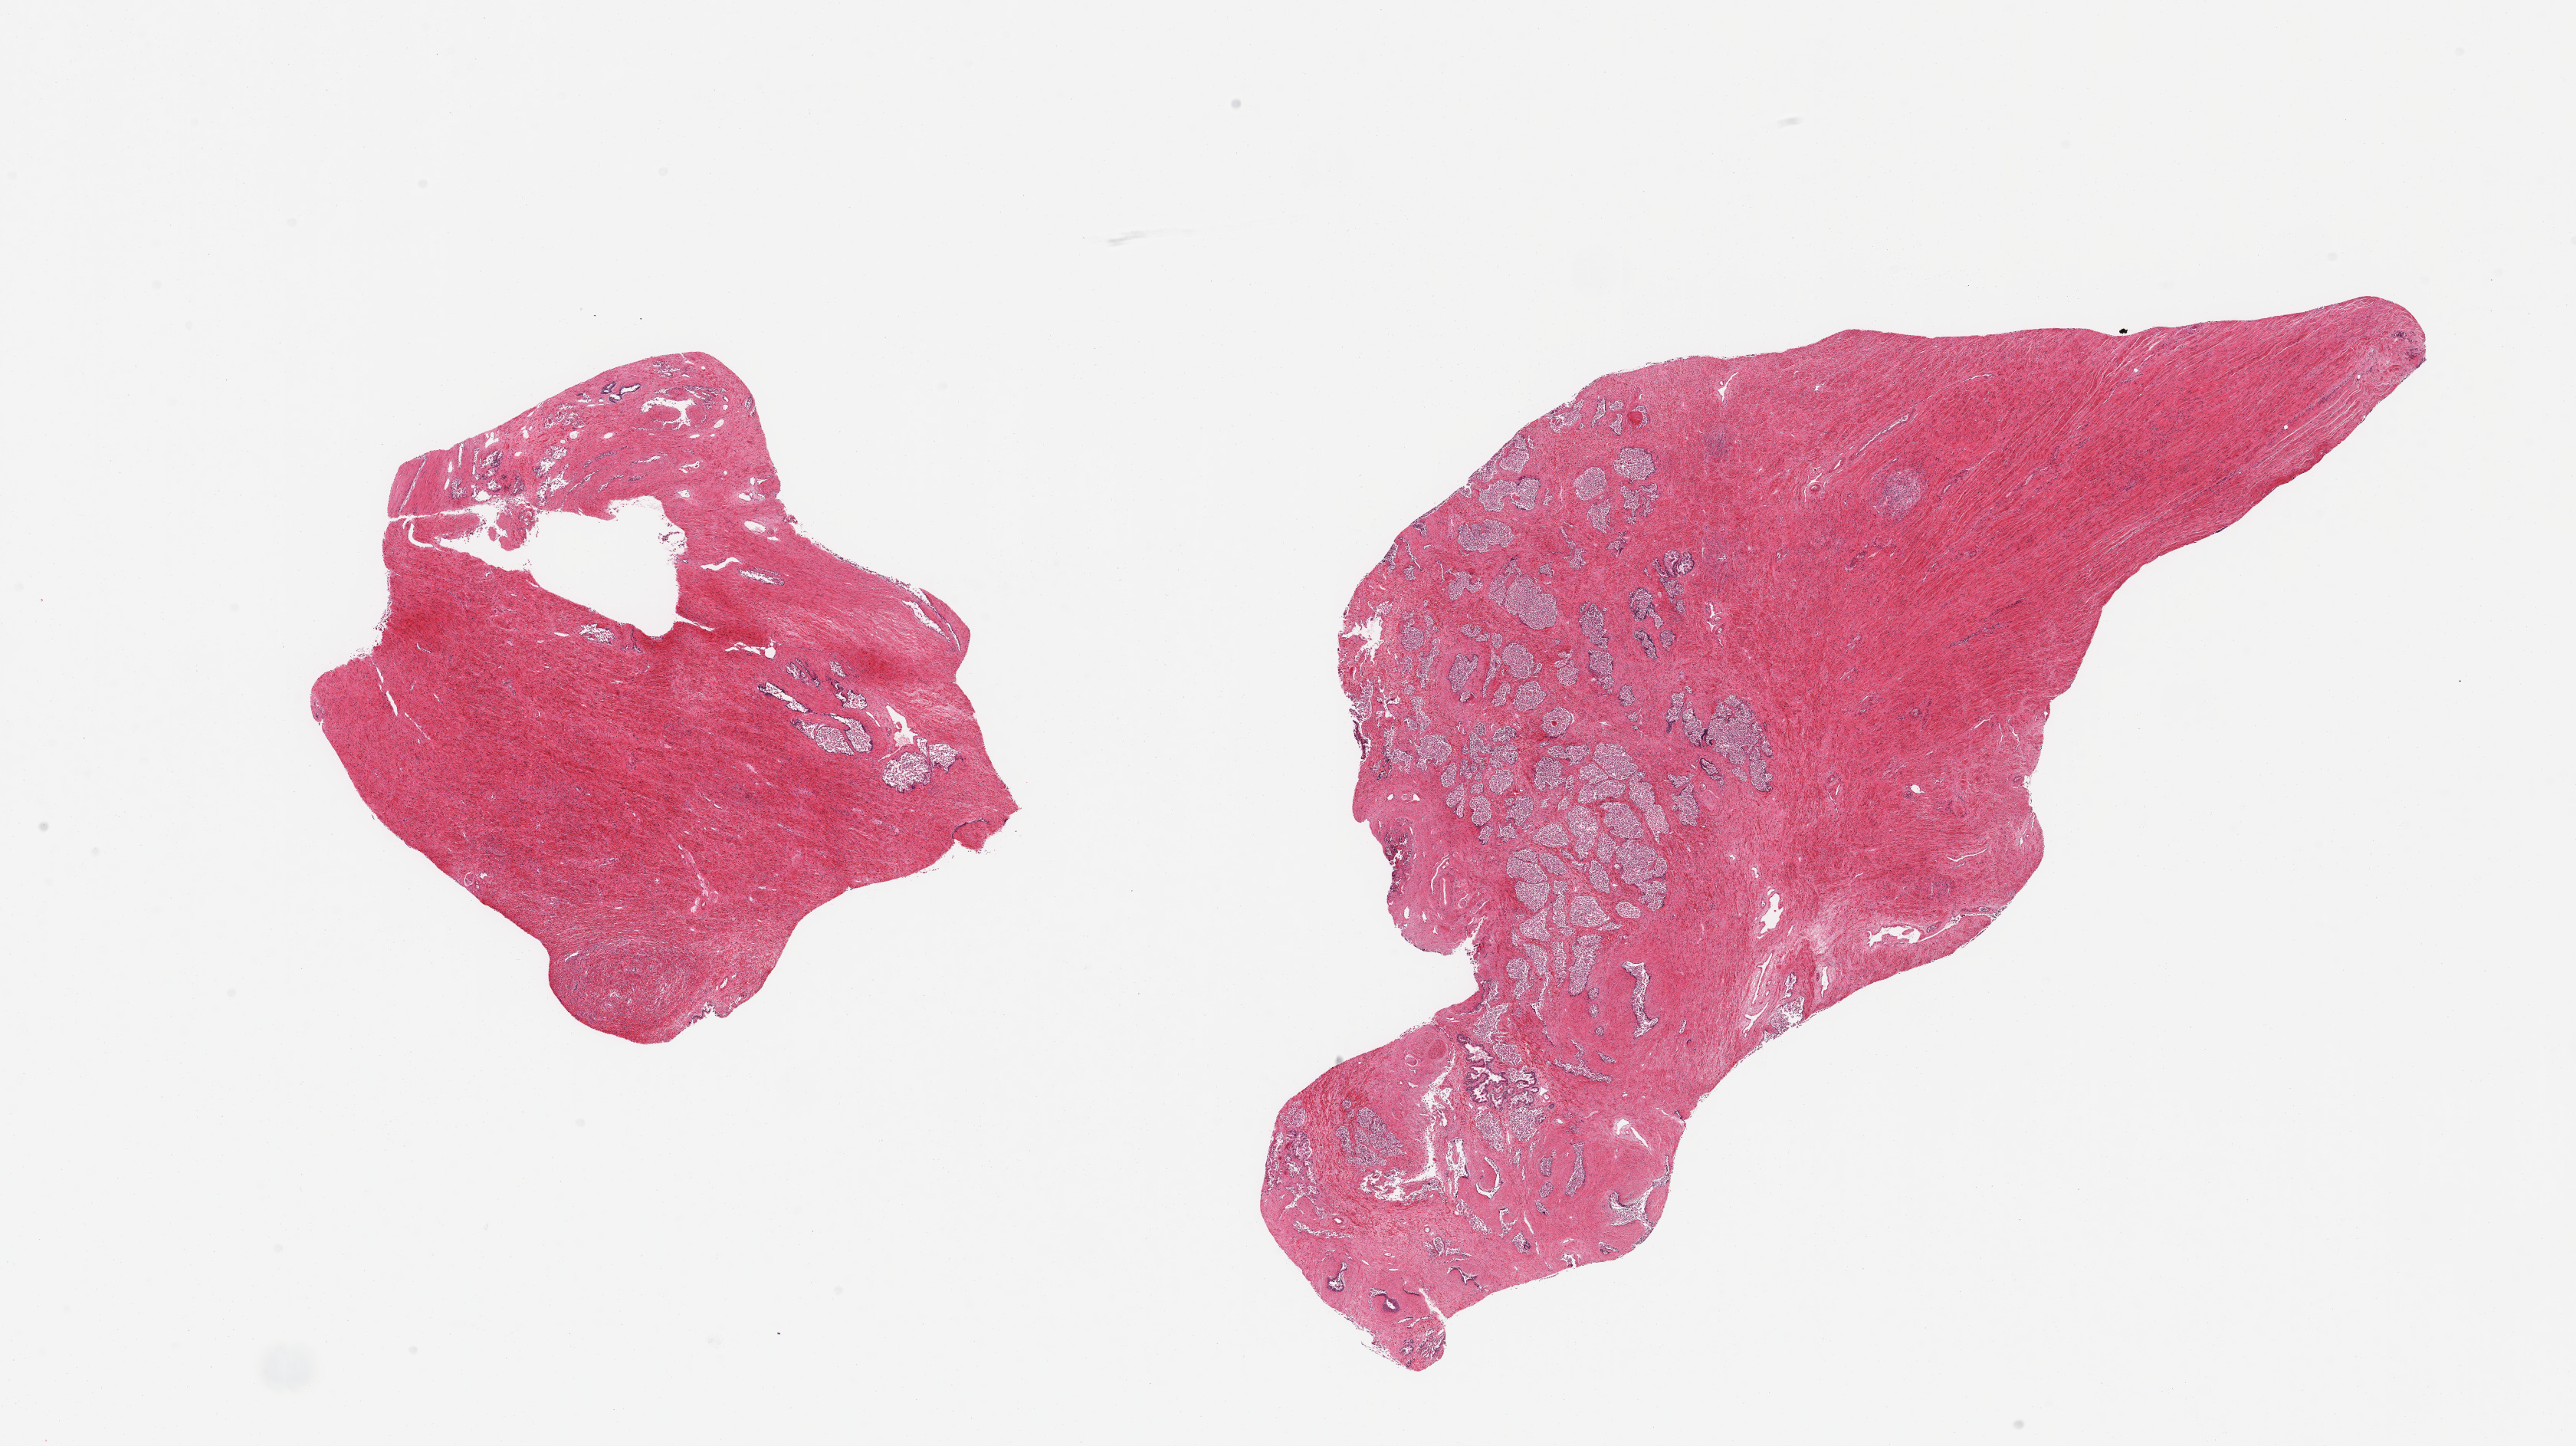
Whole-slide image, H&E stain, shown as a low-resolution overview of the whole scanned area (about 26.6 x 14.9 mm); PAXgene-fixed paraffin-embedded (PFPE) section; section of prostate (target tissue); donor tissue sample.
Pathologist's review note for this sample: 2 pieces, glandular elements completely autolyzed.